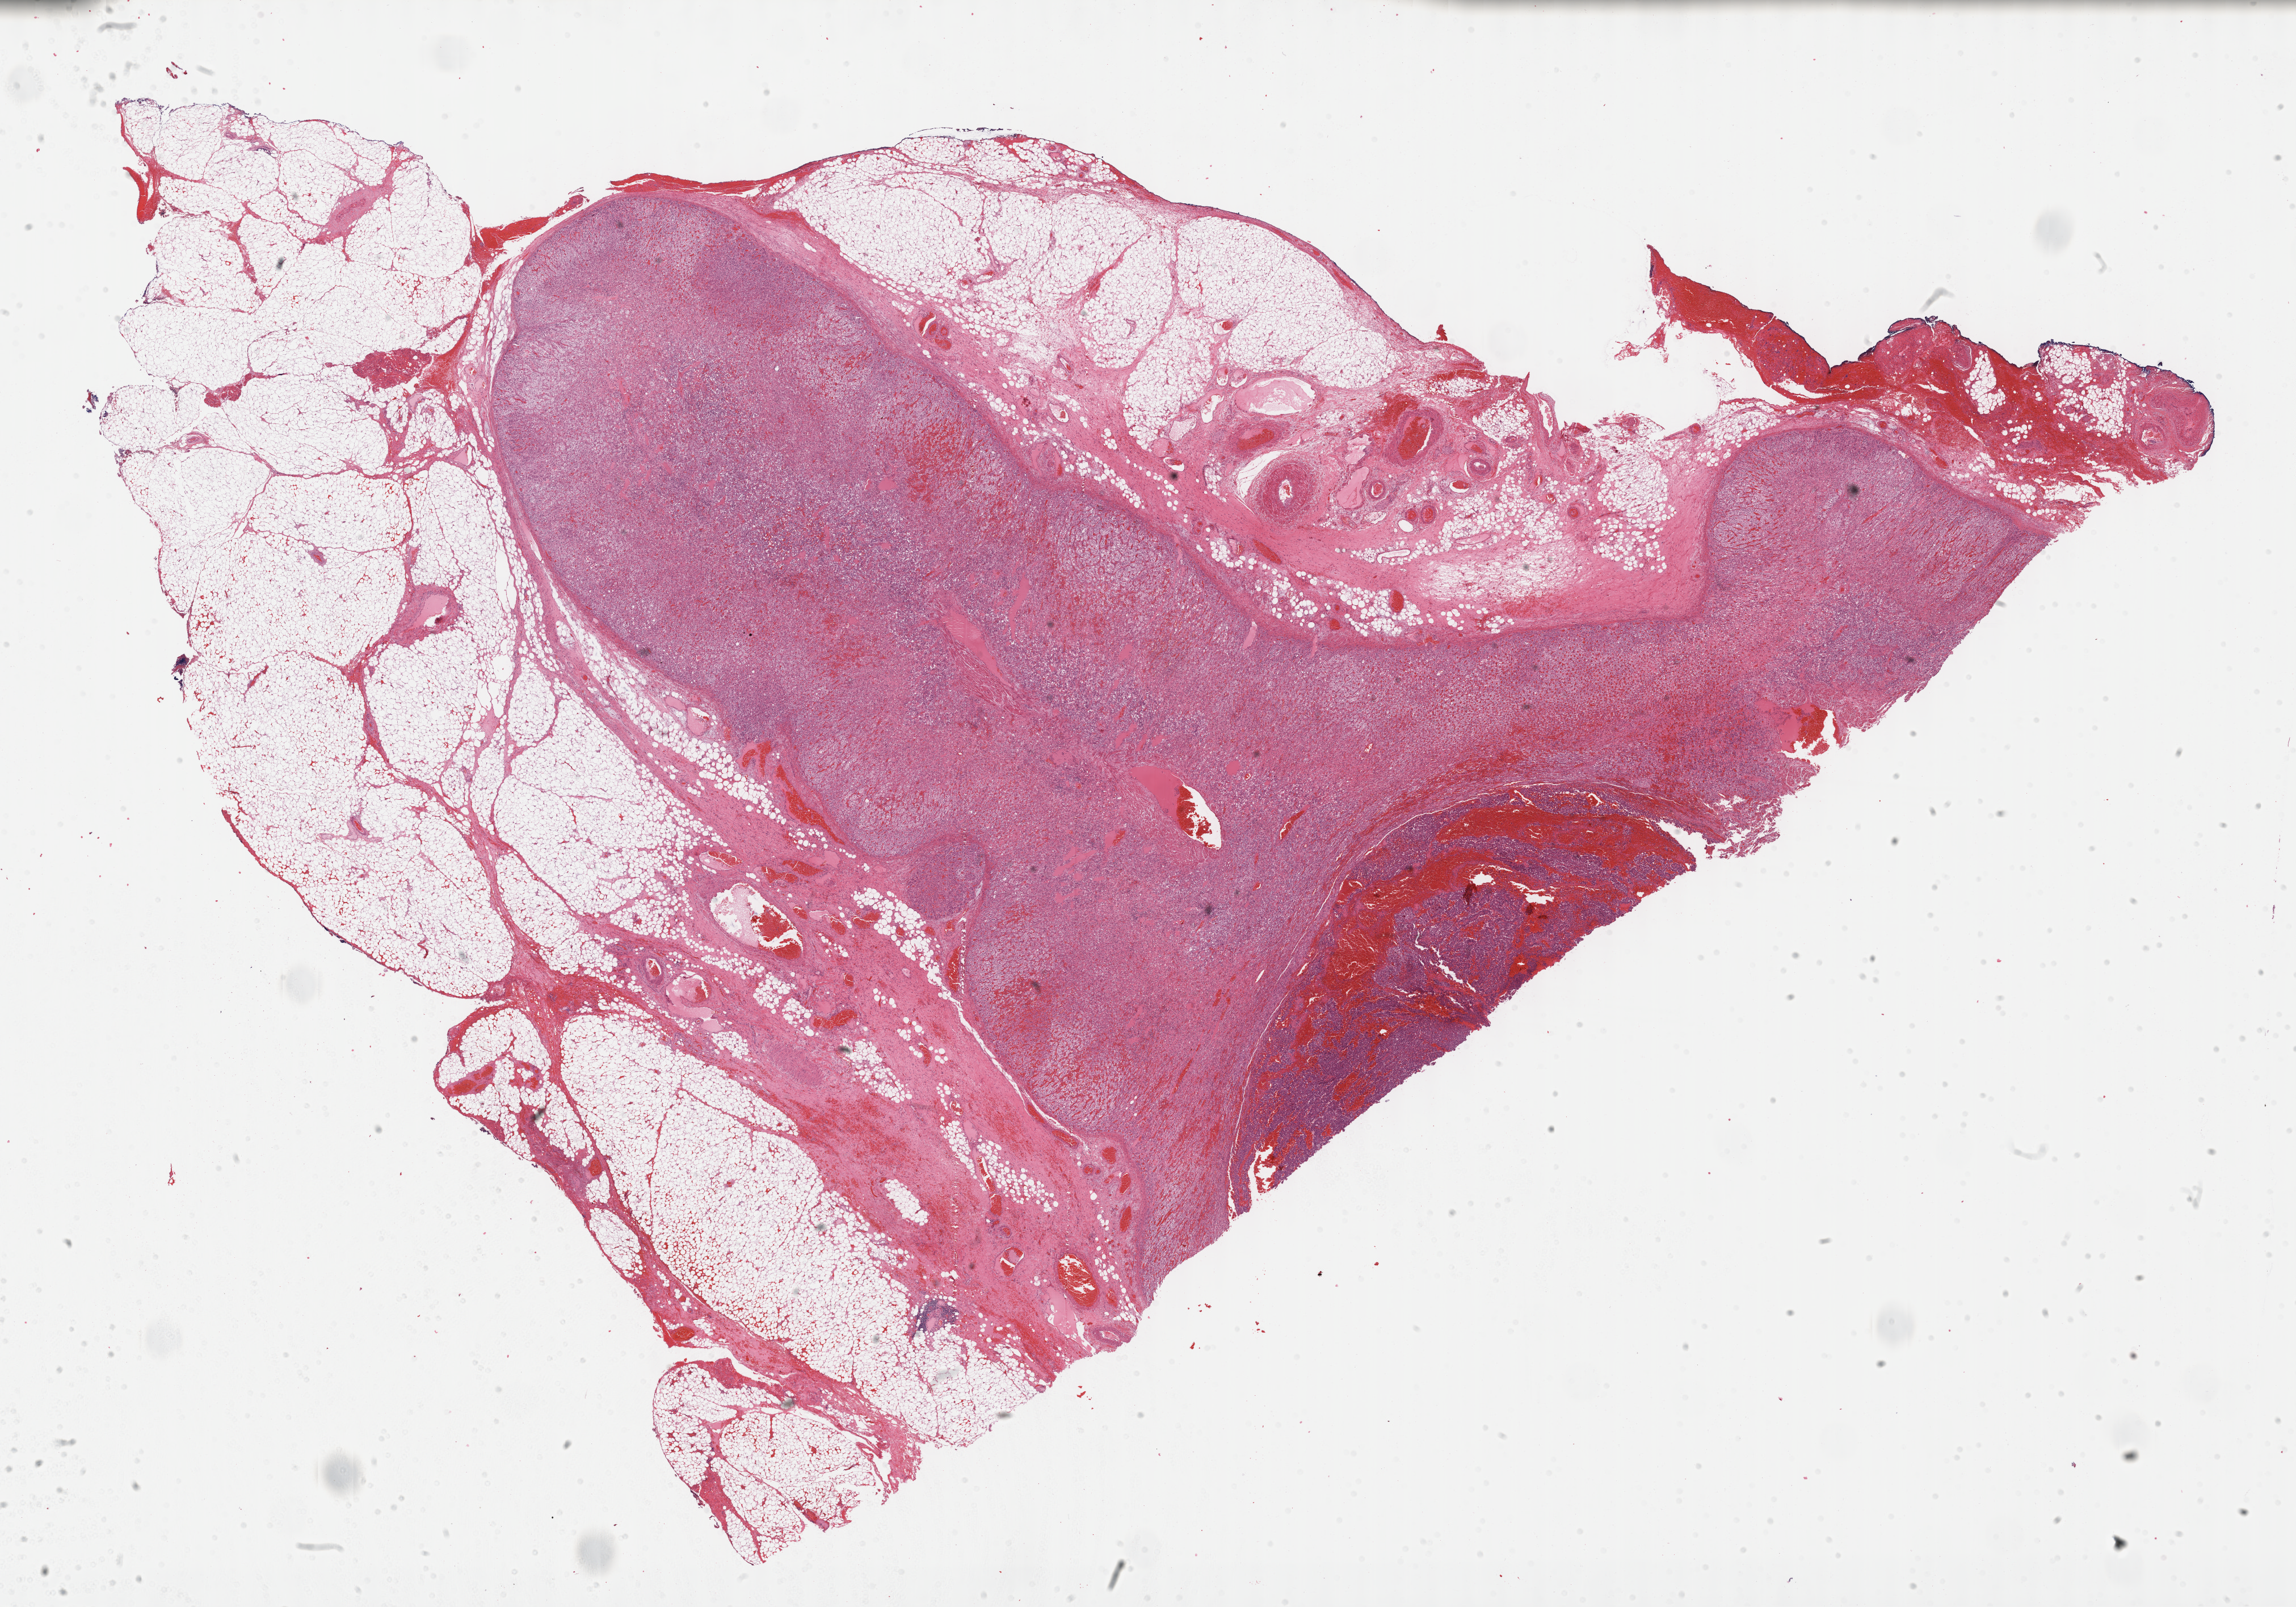
Whole-slide histology image, Hematoxylin and eosin (H&E) stained, a low-resolution overview of the entire scanned area, about 32.7 x 22.9 mm; formalin-fixed paraffin-embedded (FFPE) diagnostic section; sample: primary tumour, adrenal cortex. Male, age 52 years at initial diagnosis.
- diagnosis: Adrenal cortical carcinoma (cortex of adrenal gland)